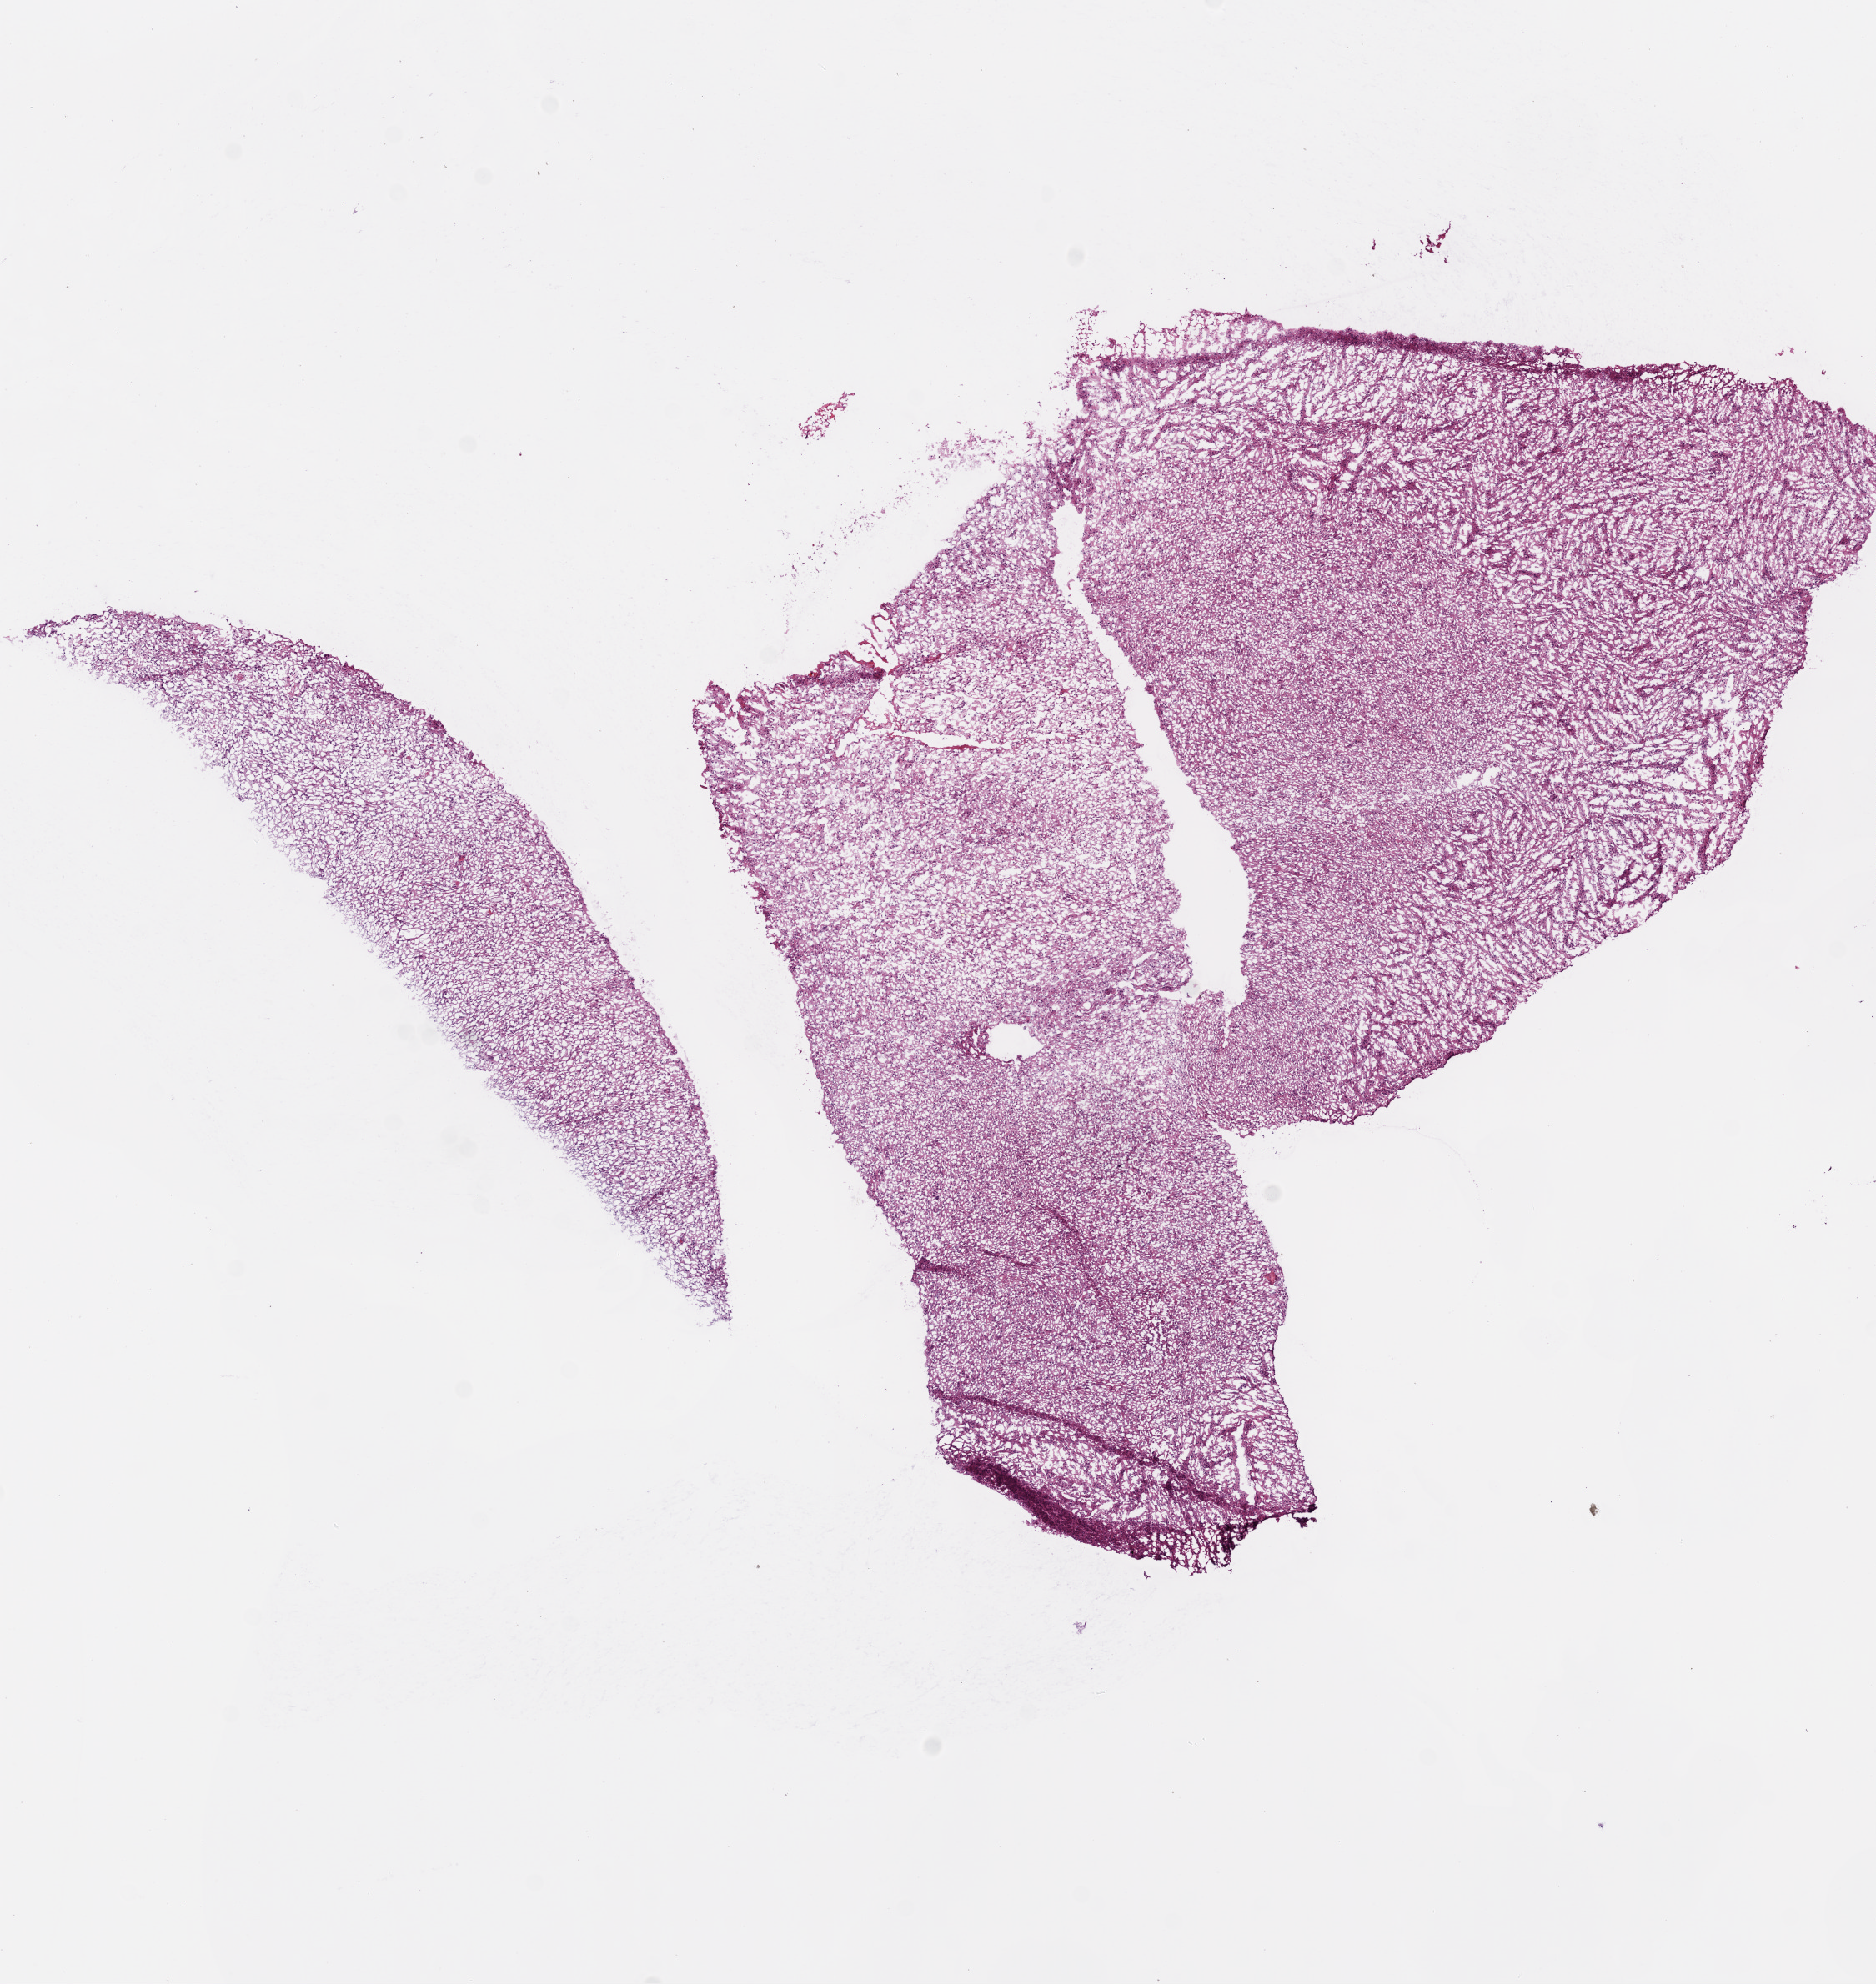
Whole-slide histology image, Hematoxylin and eosin (H&E) stained — a low-resolution overview of the entire scanned area, about 9.0 x 9.5 mm; frozen section from the bottom of the tissue portion; brain, primary tumour sample. Female, age 52 years at initial diagnosis. Composition of this section per pathologist review: tumour cells 100%, tumour nuclei 80%, normal cells 0%, stromal cells 0%, necrosis 0%.
Histologic diagnosis: Glioblastoma.